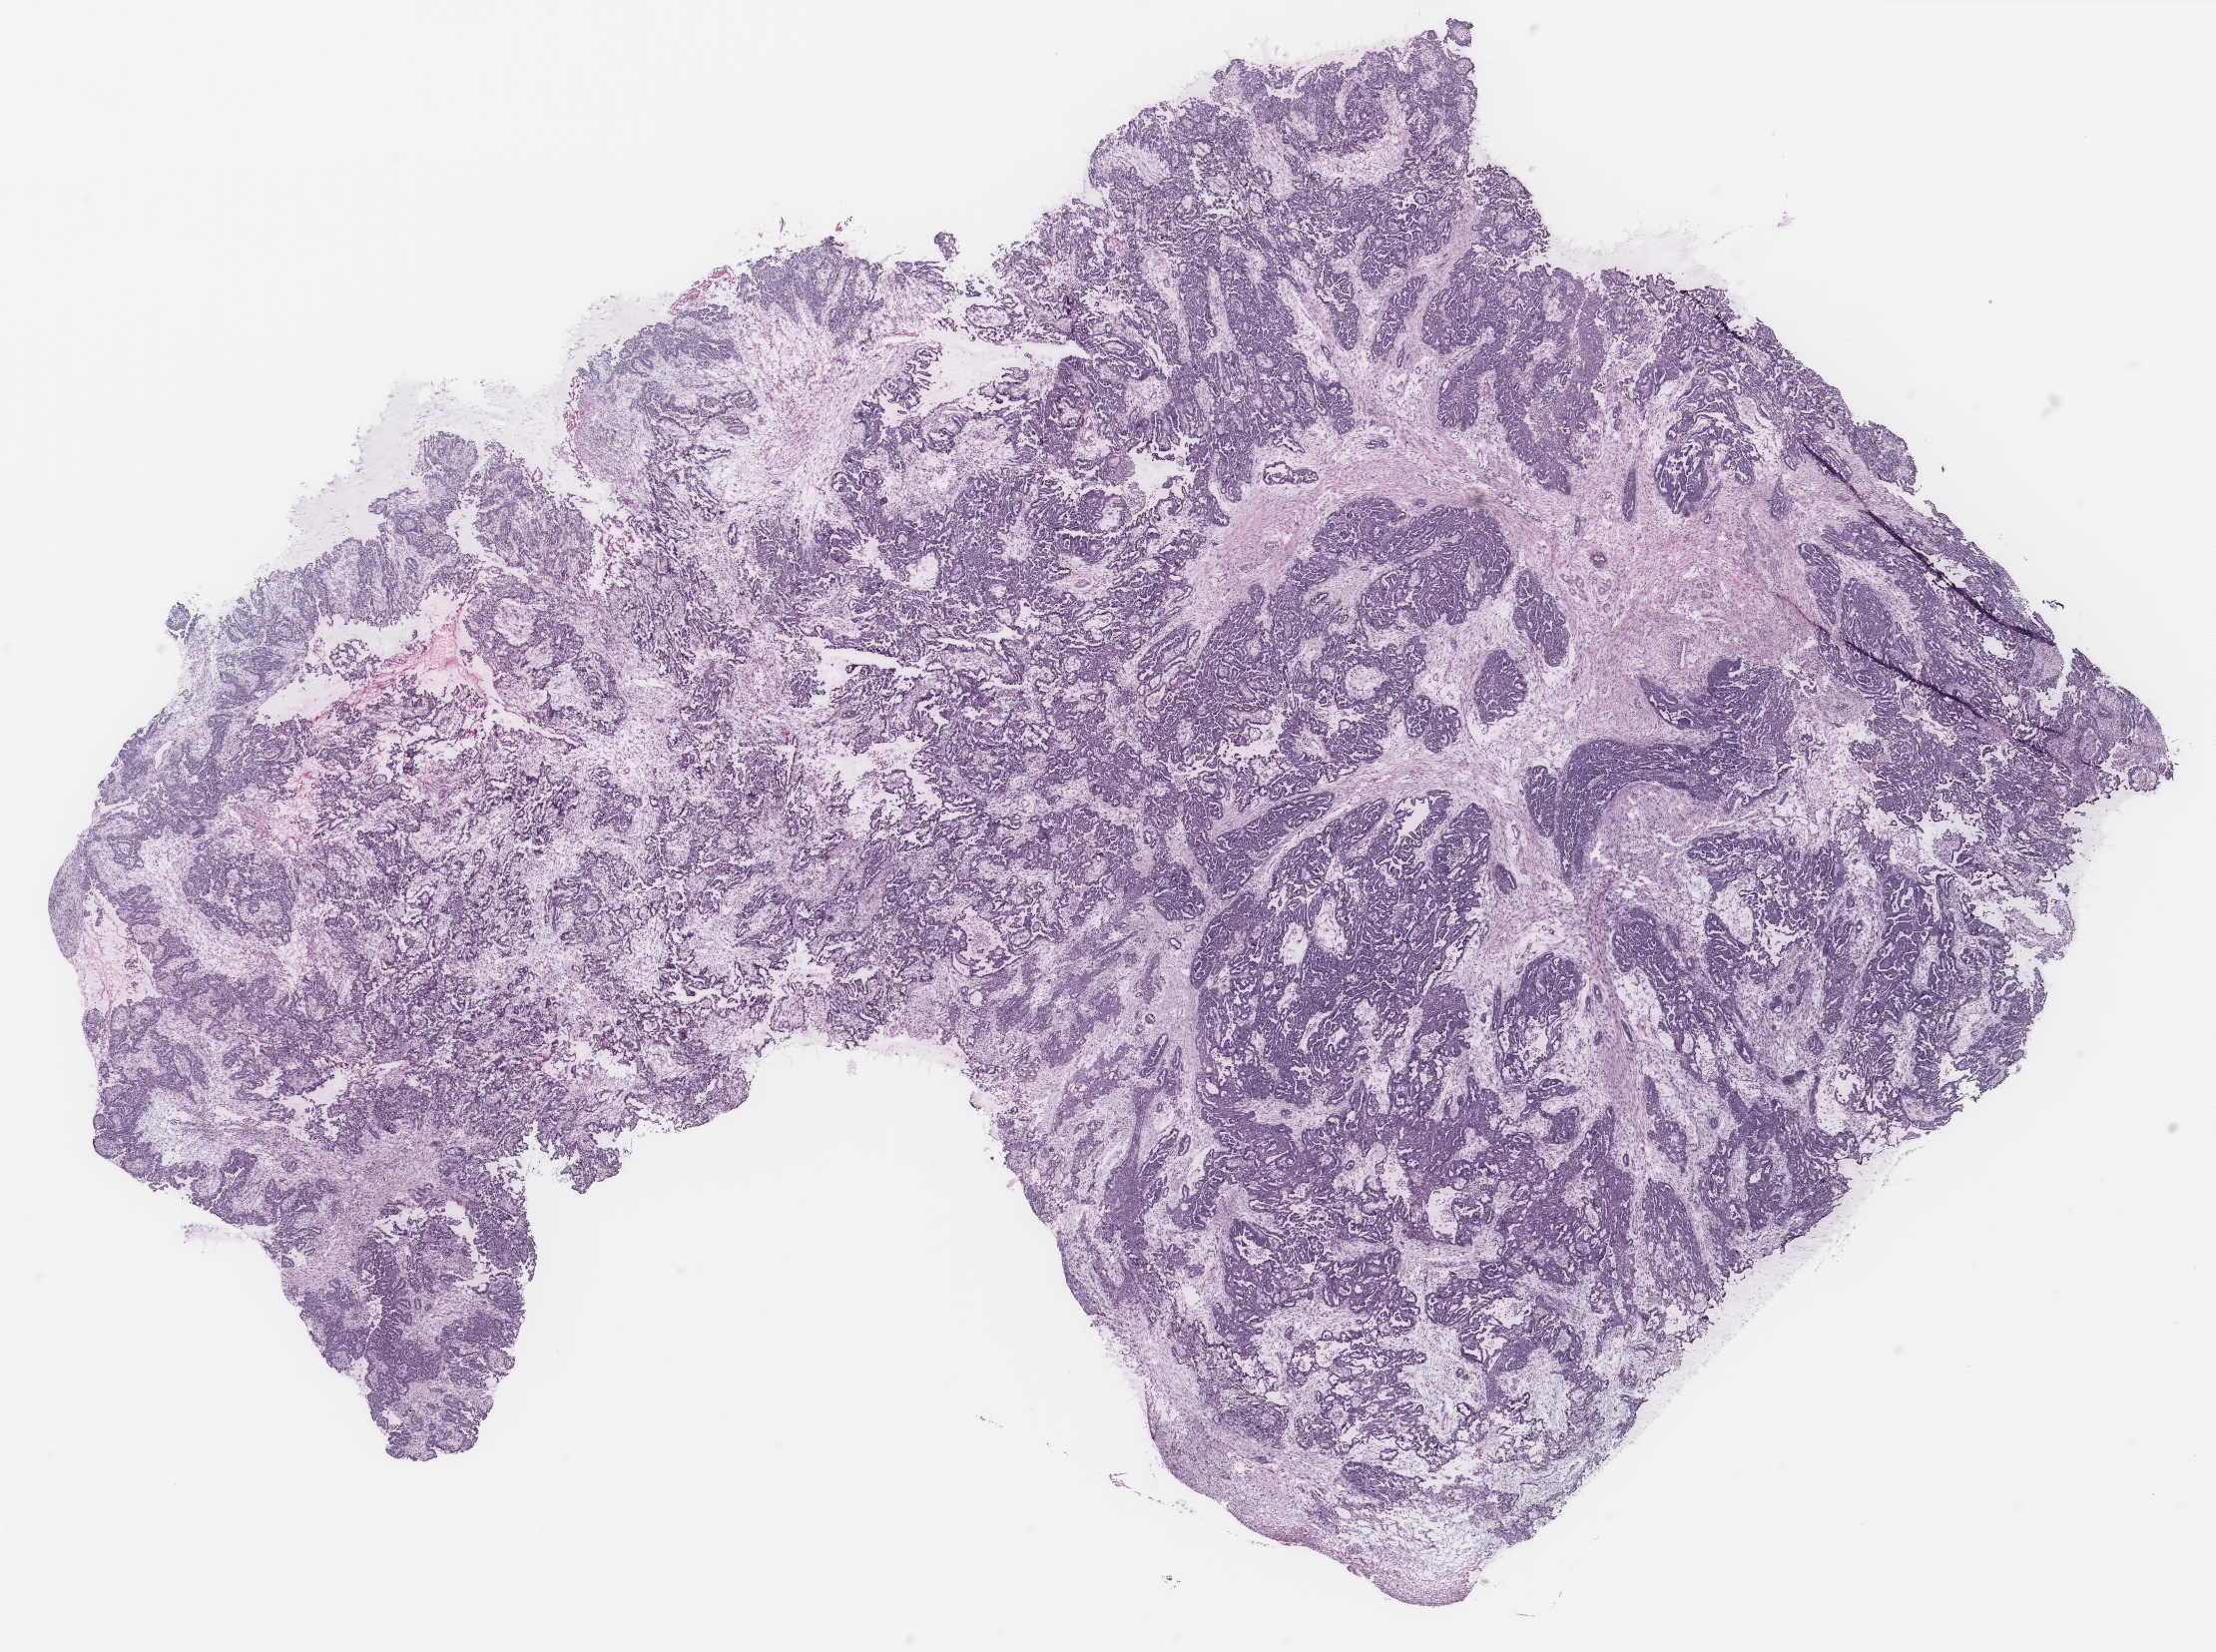
H&E-stained whole-slide image — a low-resolution overview of the entire scanned area, about 17.8 x 13.2 mm (slide scanned at 40x), ovary, tumour tissue. 50-year-old female patient.
Histologic diagnosis: Serous adenocarcinoma, NOS.